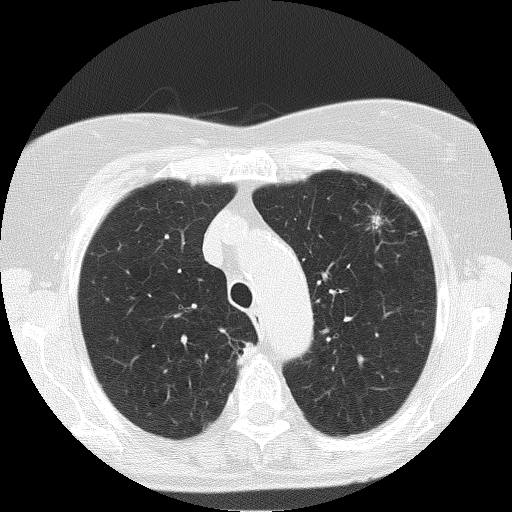
Low-dose screening chest CT, one axial slice; slice 131 of 166 in the series (ordered by position); reconstruction kernel FC51; lung window (W 1500 / L -600 HU); 2 mm slice thickness; 512 × 512 image matrix, field of view 303 × 303 mm.
Outlined on this slice (outlined manually by an expert reader):
- lesion 1 (tumor, upper lobe of left lung): bounding box <373,215,381,227> (left, top, right, bottom; pixels)